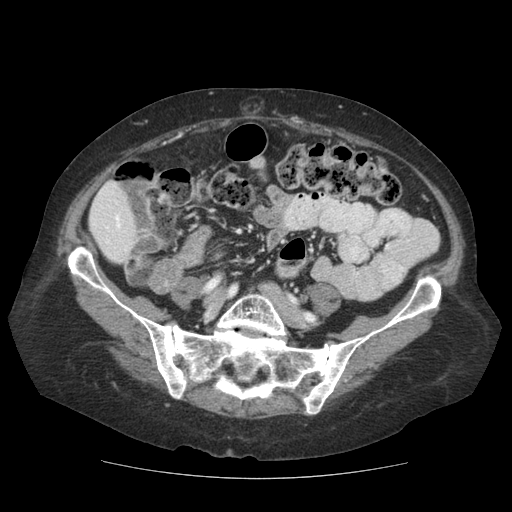
Contrast-enhanced abdominal CT (liver protocol), one axial slice. Position 18 of 111 along the scan axis. 140 kVp. Soft-tissue window (W 400 / L 40 HU). 2.5 mm slice thickness. 512 × 512 image matrix. Case-level facts recorded for this patient, not image findings: diagnosis: hepatocellular carcinoma (patient treated with transarterial chemoembolisation; whether this scan precedes or follows treatment is not stated here); TNM stage (as recorded): Stage-I.
Structures marked on this image (semi-automatic segmentation, software-assisted and operator-edited):
- liver parenchyma outside the tumour (the mass and vessels are separate outlines, so this box may not span the whole liver): bounding box (x1, y1, x2, y2) in pixels: (88, 181, 136, 262)
- liver vessels: (115, 215, 120, 228)